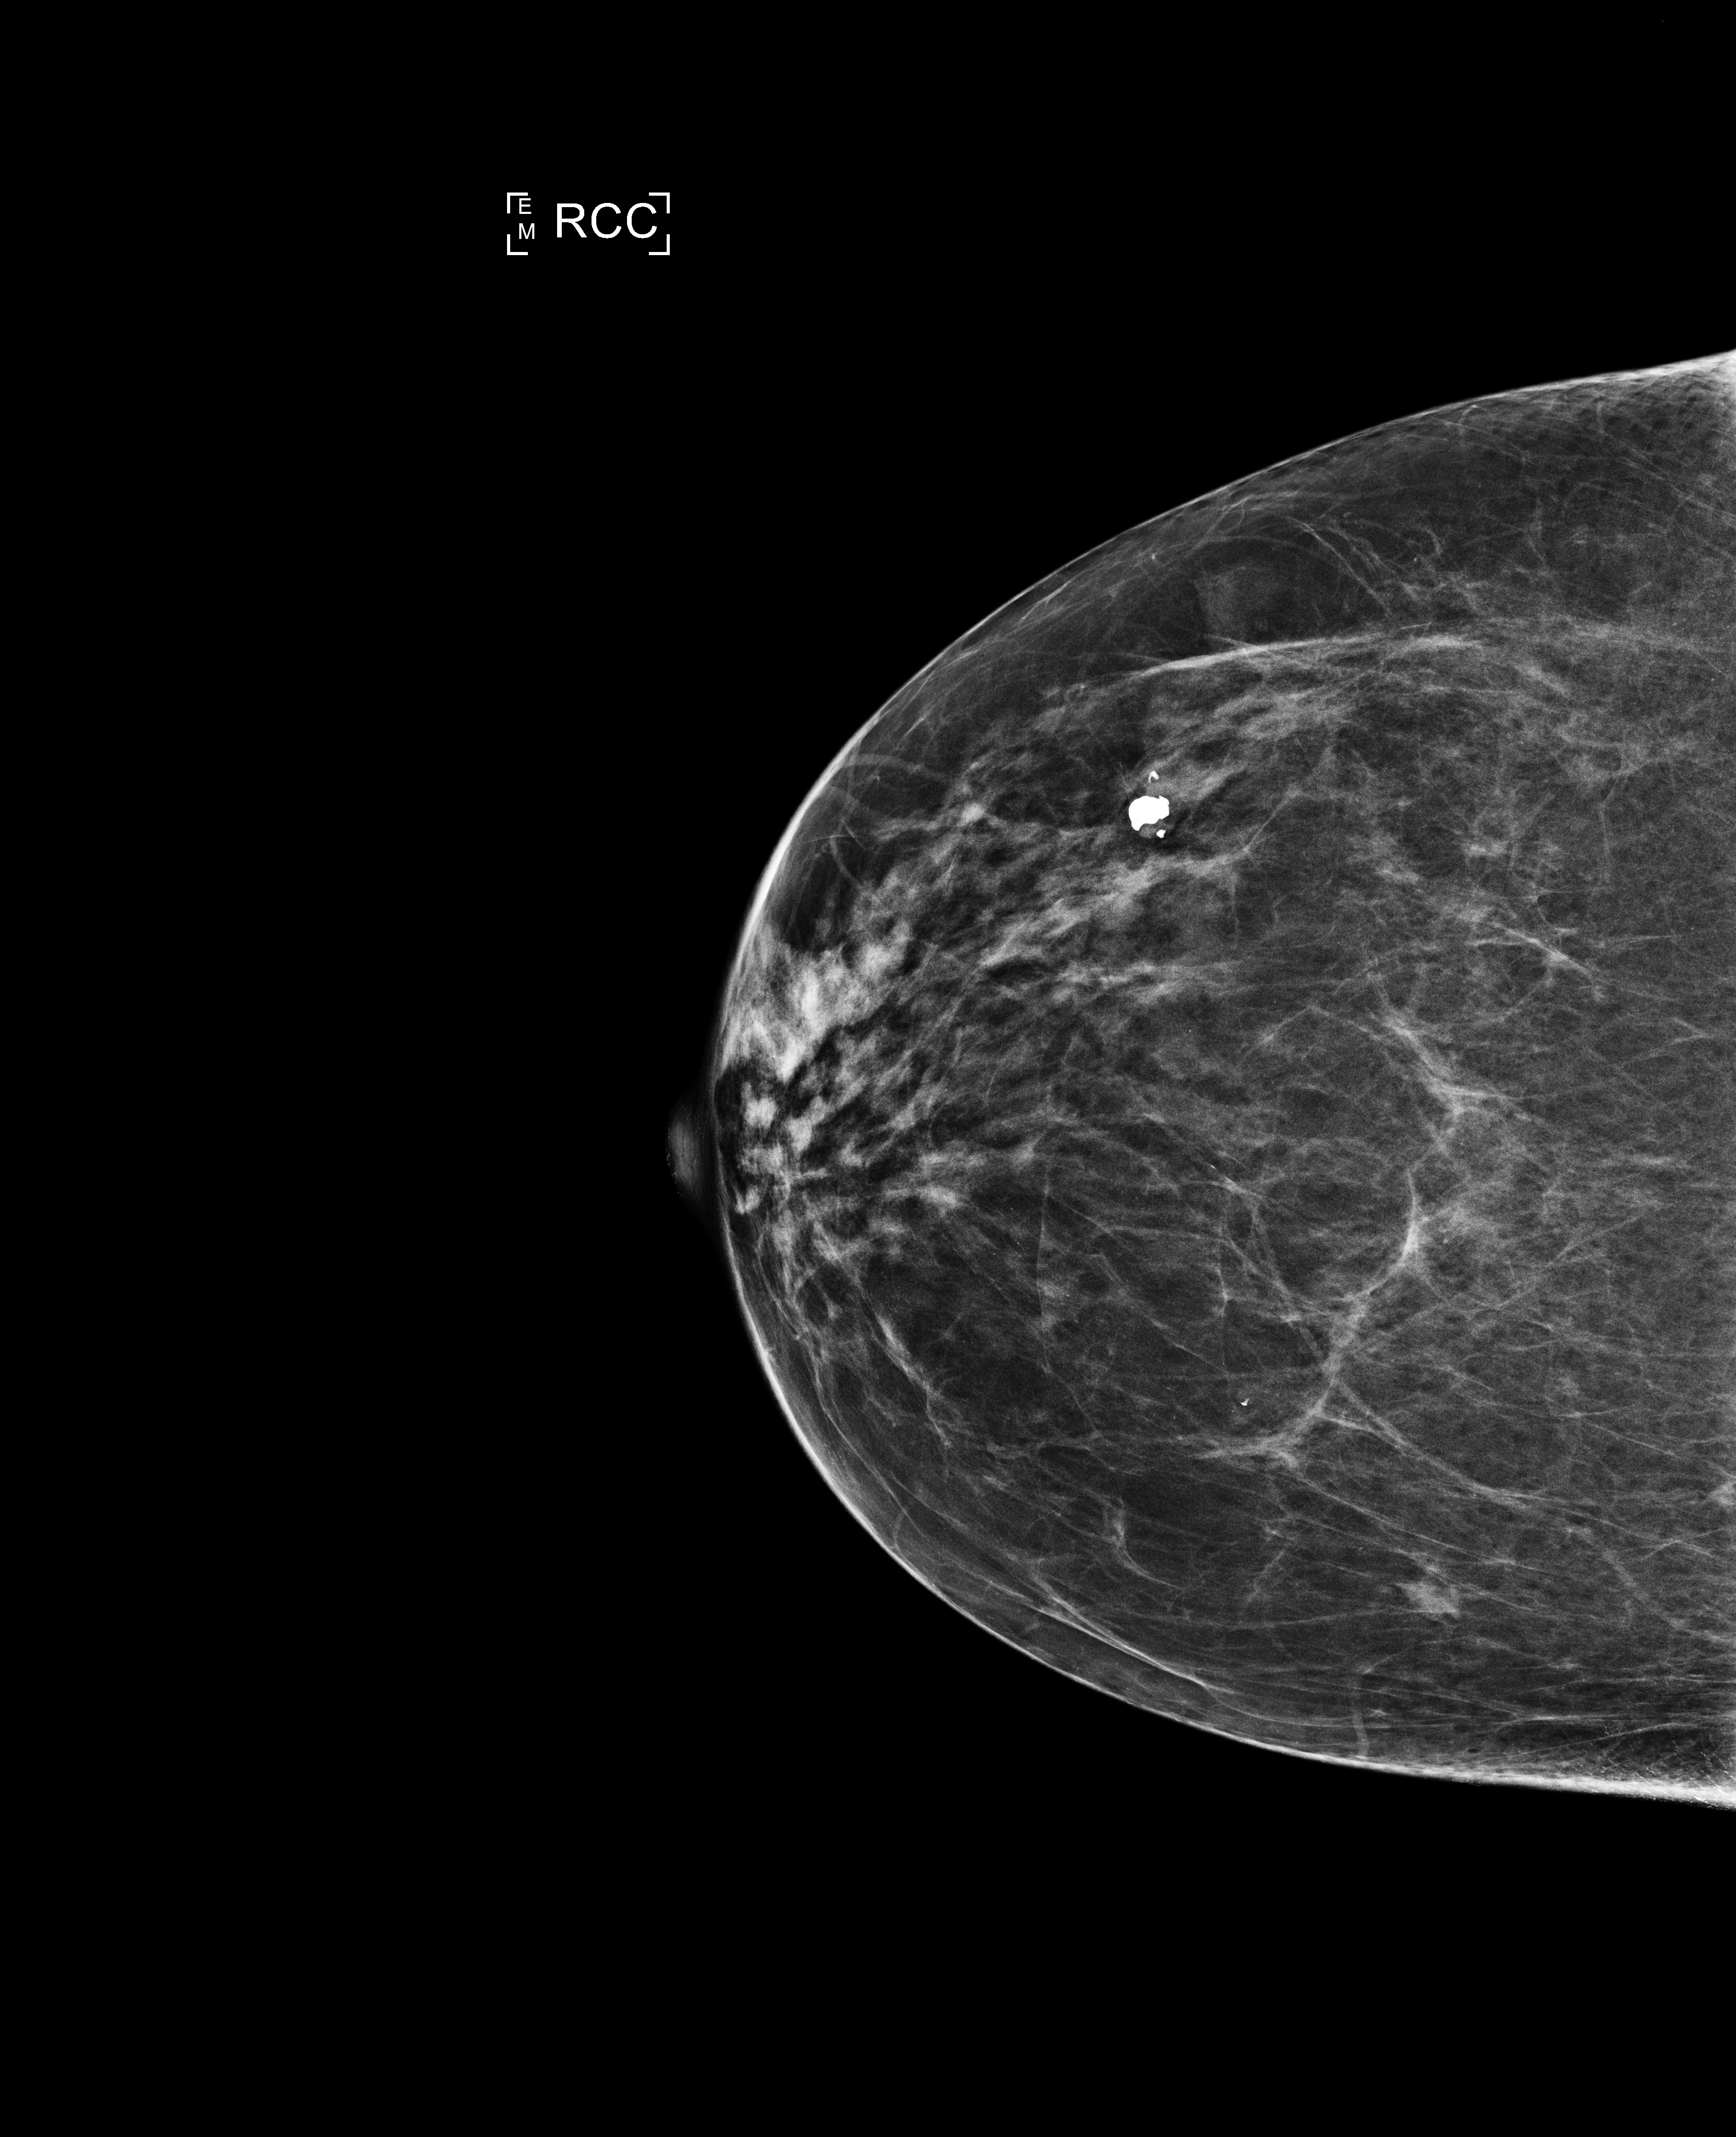
Screening examination, compressed breast thickness 55 mm. Patient aged 64 years (female).
Image type: full-field digital mammogram. Breast: right. Projection: cranio-caudal projection.